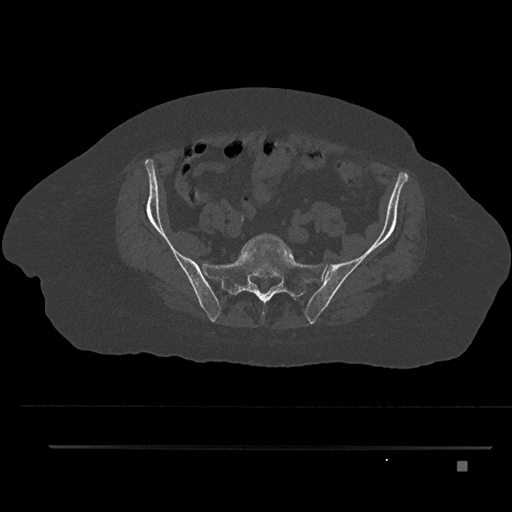
CT including the spine, one axial slice; slice 5 of 797 in the series (ordered by position); 120 kVp; bone window (W 1800 / L 400 HU); 512 × 512 image matrix, field of view 437 × 437 mm. Patient: female, 76 years. From the clinical record (not read from this slice): primary cancer: lung; vertebrae with lytic lesions (as recorded): T11, L3.
Annotated regions visible in this slice (semi-automatic segmentation, software-assisted and operator-edited):
- L5 vertebra: bounding box [x1, y1, x2, y2] px = [242, 233, 293, 258]